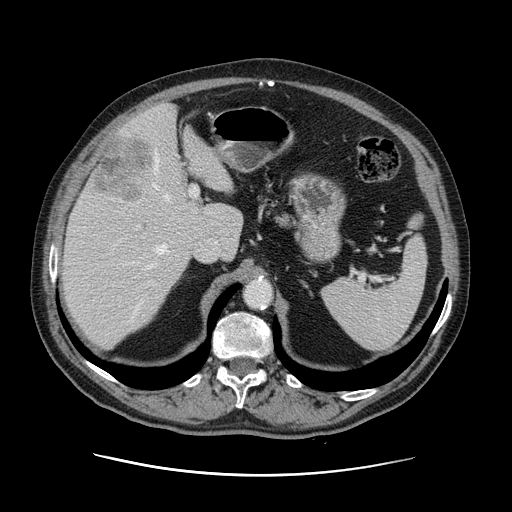
Contrast-enhanced abdominal CT, one axial slice; slice 85 of 141 in the series (ordered by position); soft-tissue window (W 400 / L 40 HU); 2.5 mm slice thickness; 512 × 512 image matrix. Male patient, age 72 years. Case-level facts recorded for this patient, not image findings: diagnosis: colorectal cancer liver metastases, imaged before liver resection; multiple liver metastases: yes; largest metastasis: 5.4 cm; disease in both lobes: yes.
Outlined on this slice (expert manual segmentation):
- hepatic veins: bounding box (x1, y1, x2, y2) in pixels: (137, 156, 170, 310)
- liver: (61, 105, 243, 347)
- planned liver remnant (the part of the liver to remain after resection): (61, 108, 243, 347)
- portal vein (with intrahepatic branches): (132, 186, 198, 238)
- liver metastasis: (96, 139, 153, 200)